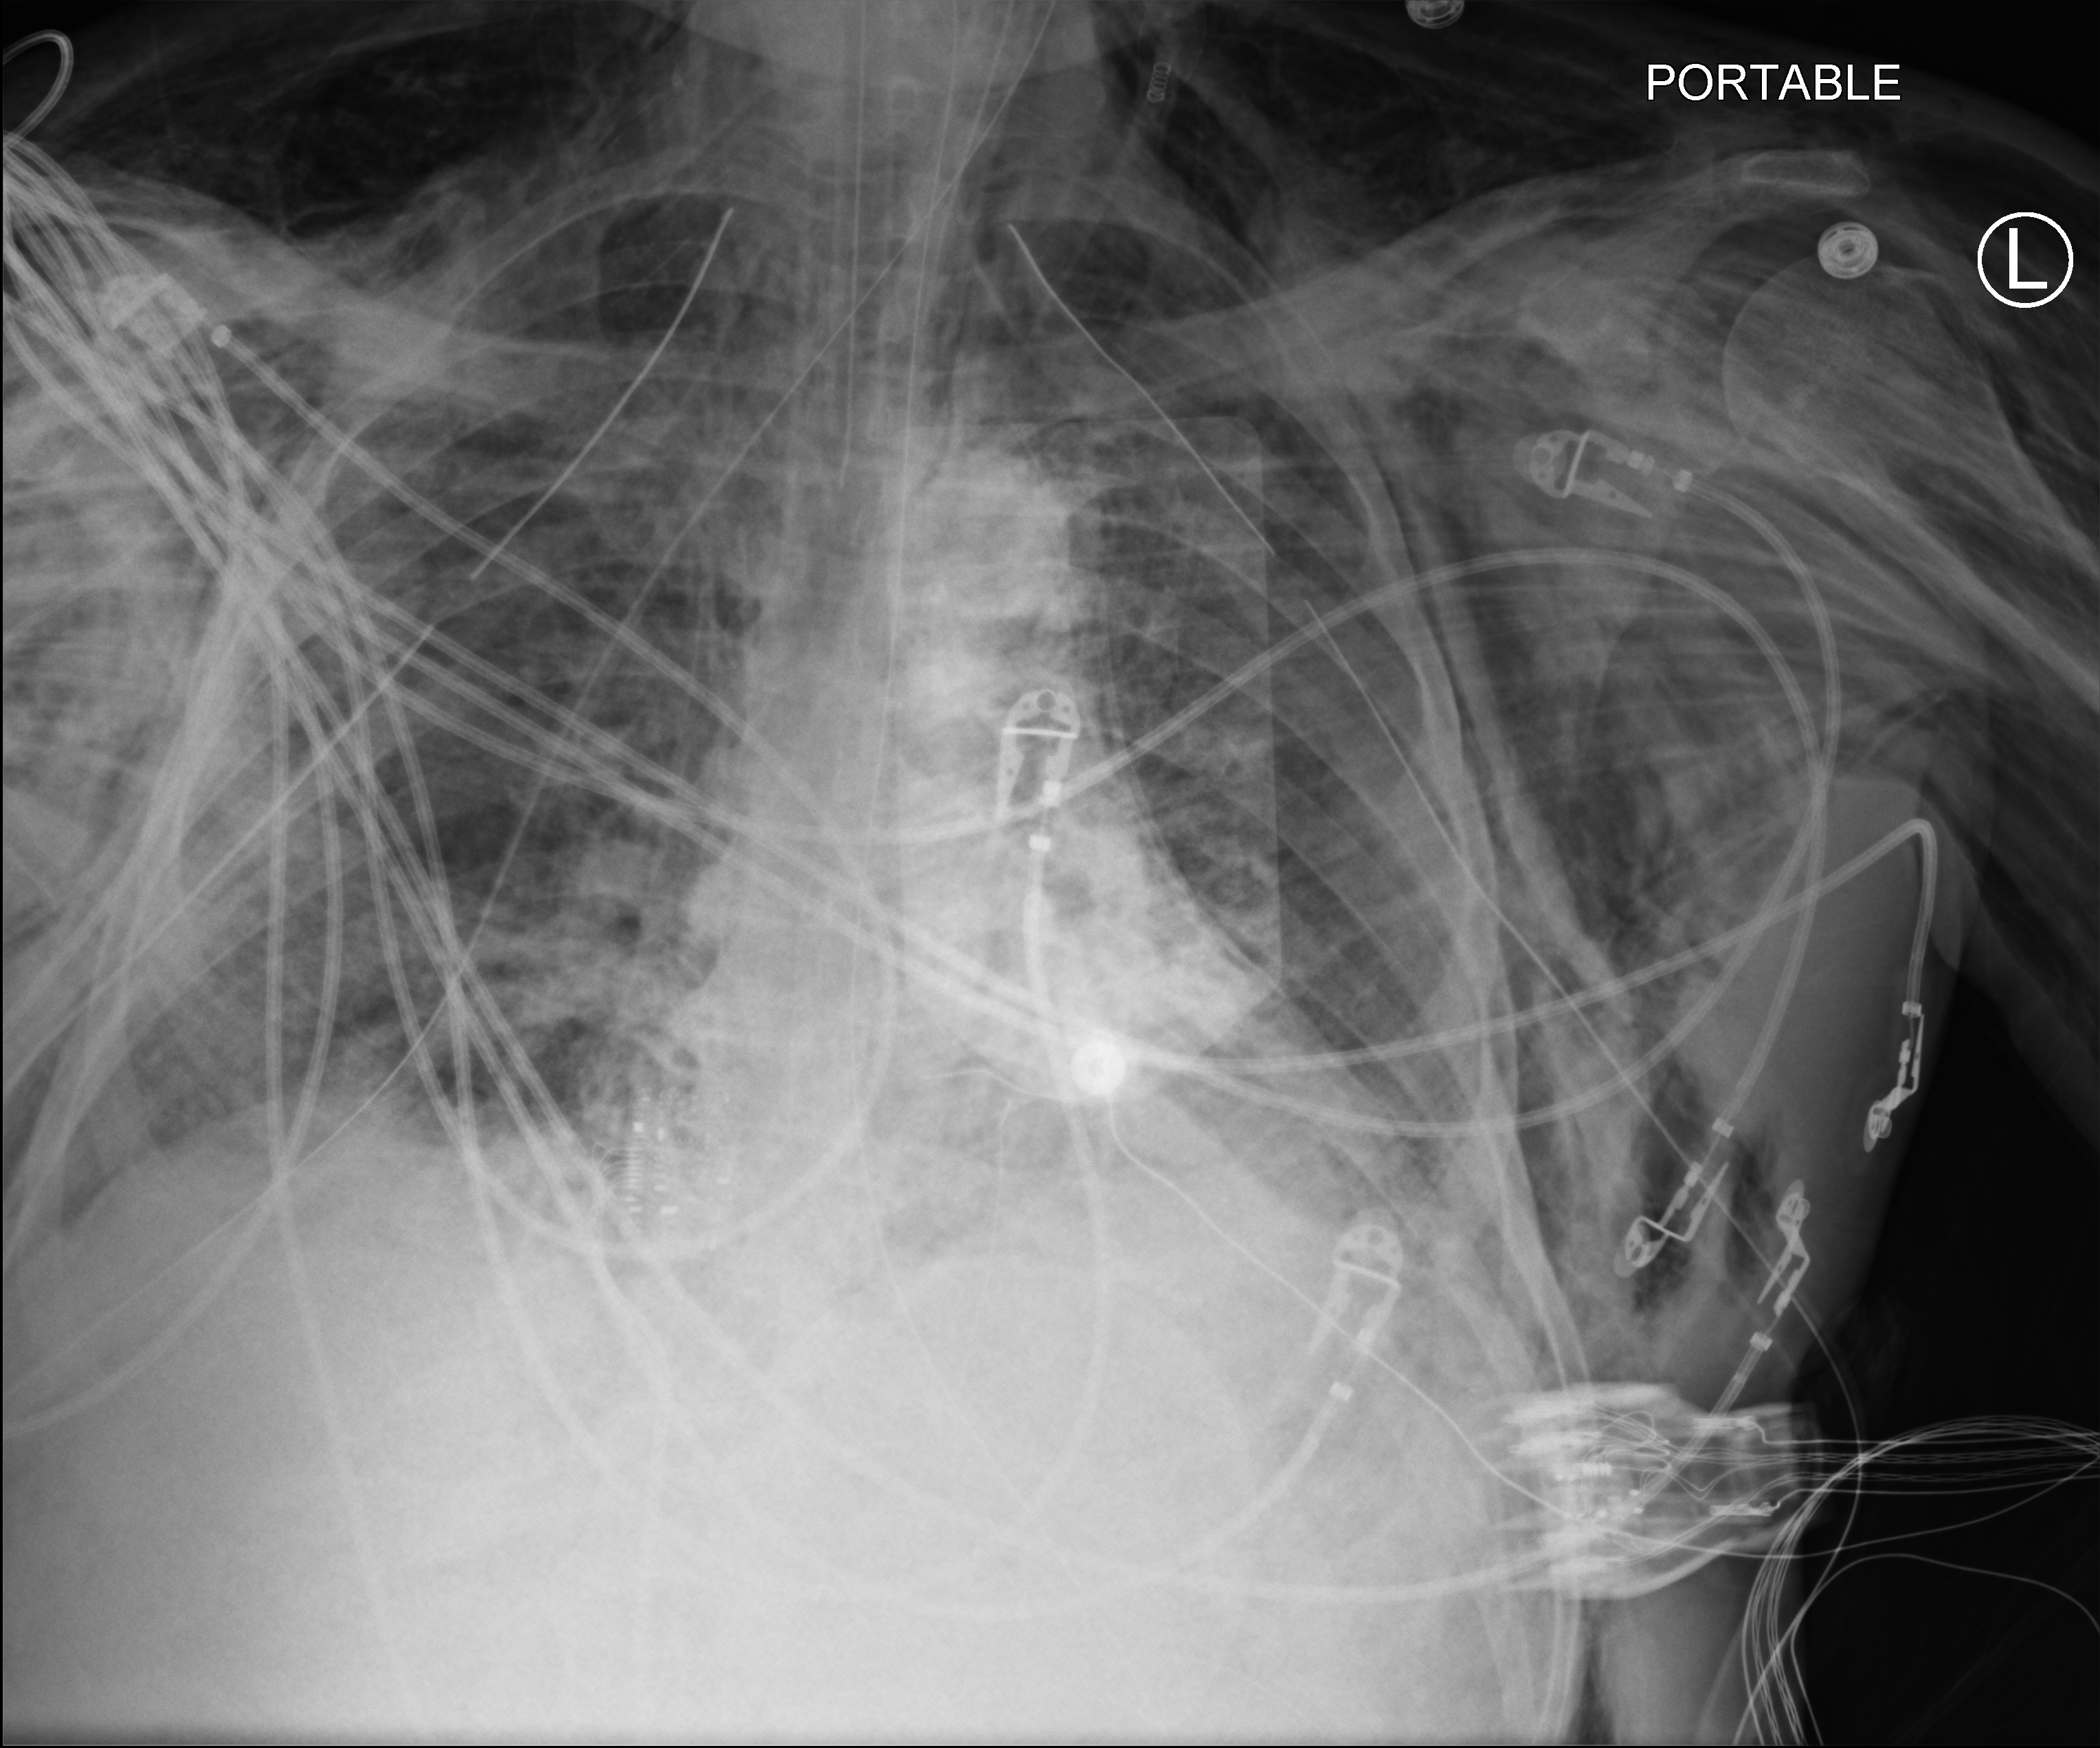
Chest X-ray (portable), anteroposterior (AP) projection. Patient hospitalised with COVID-19; male, aged 18–59 years.
Admission-level facts for this patient (not findings on this image; timing relative to this image not recorded): mechanically ventilated during this hospital stay: yes.